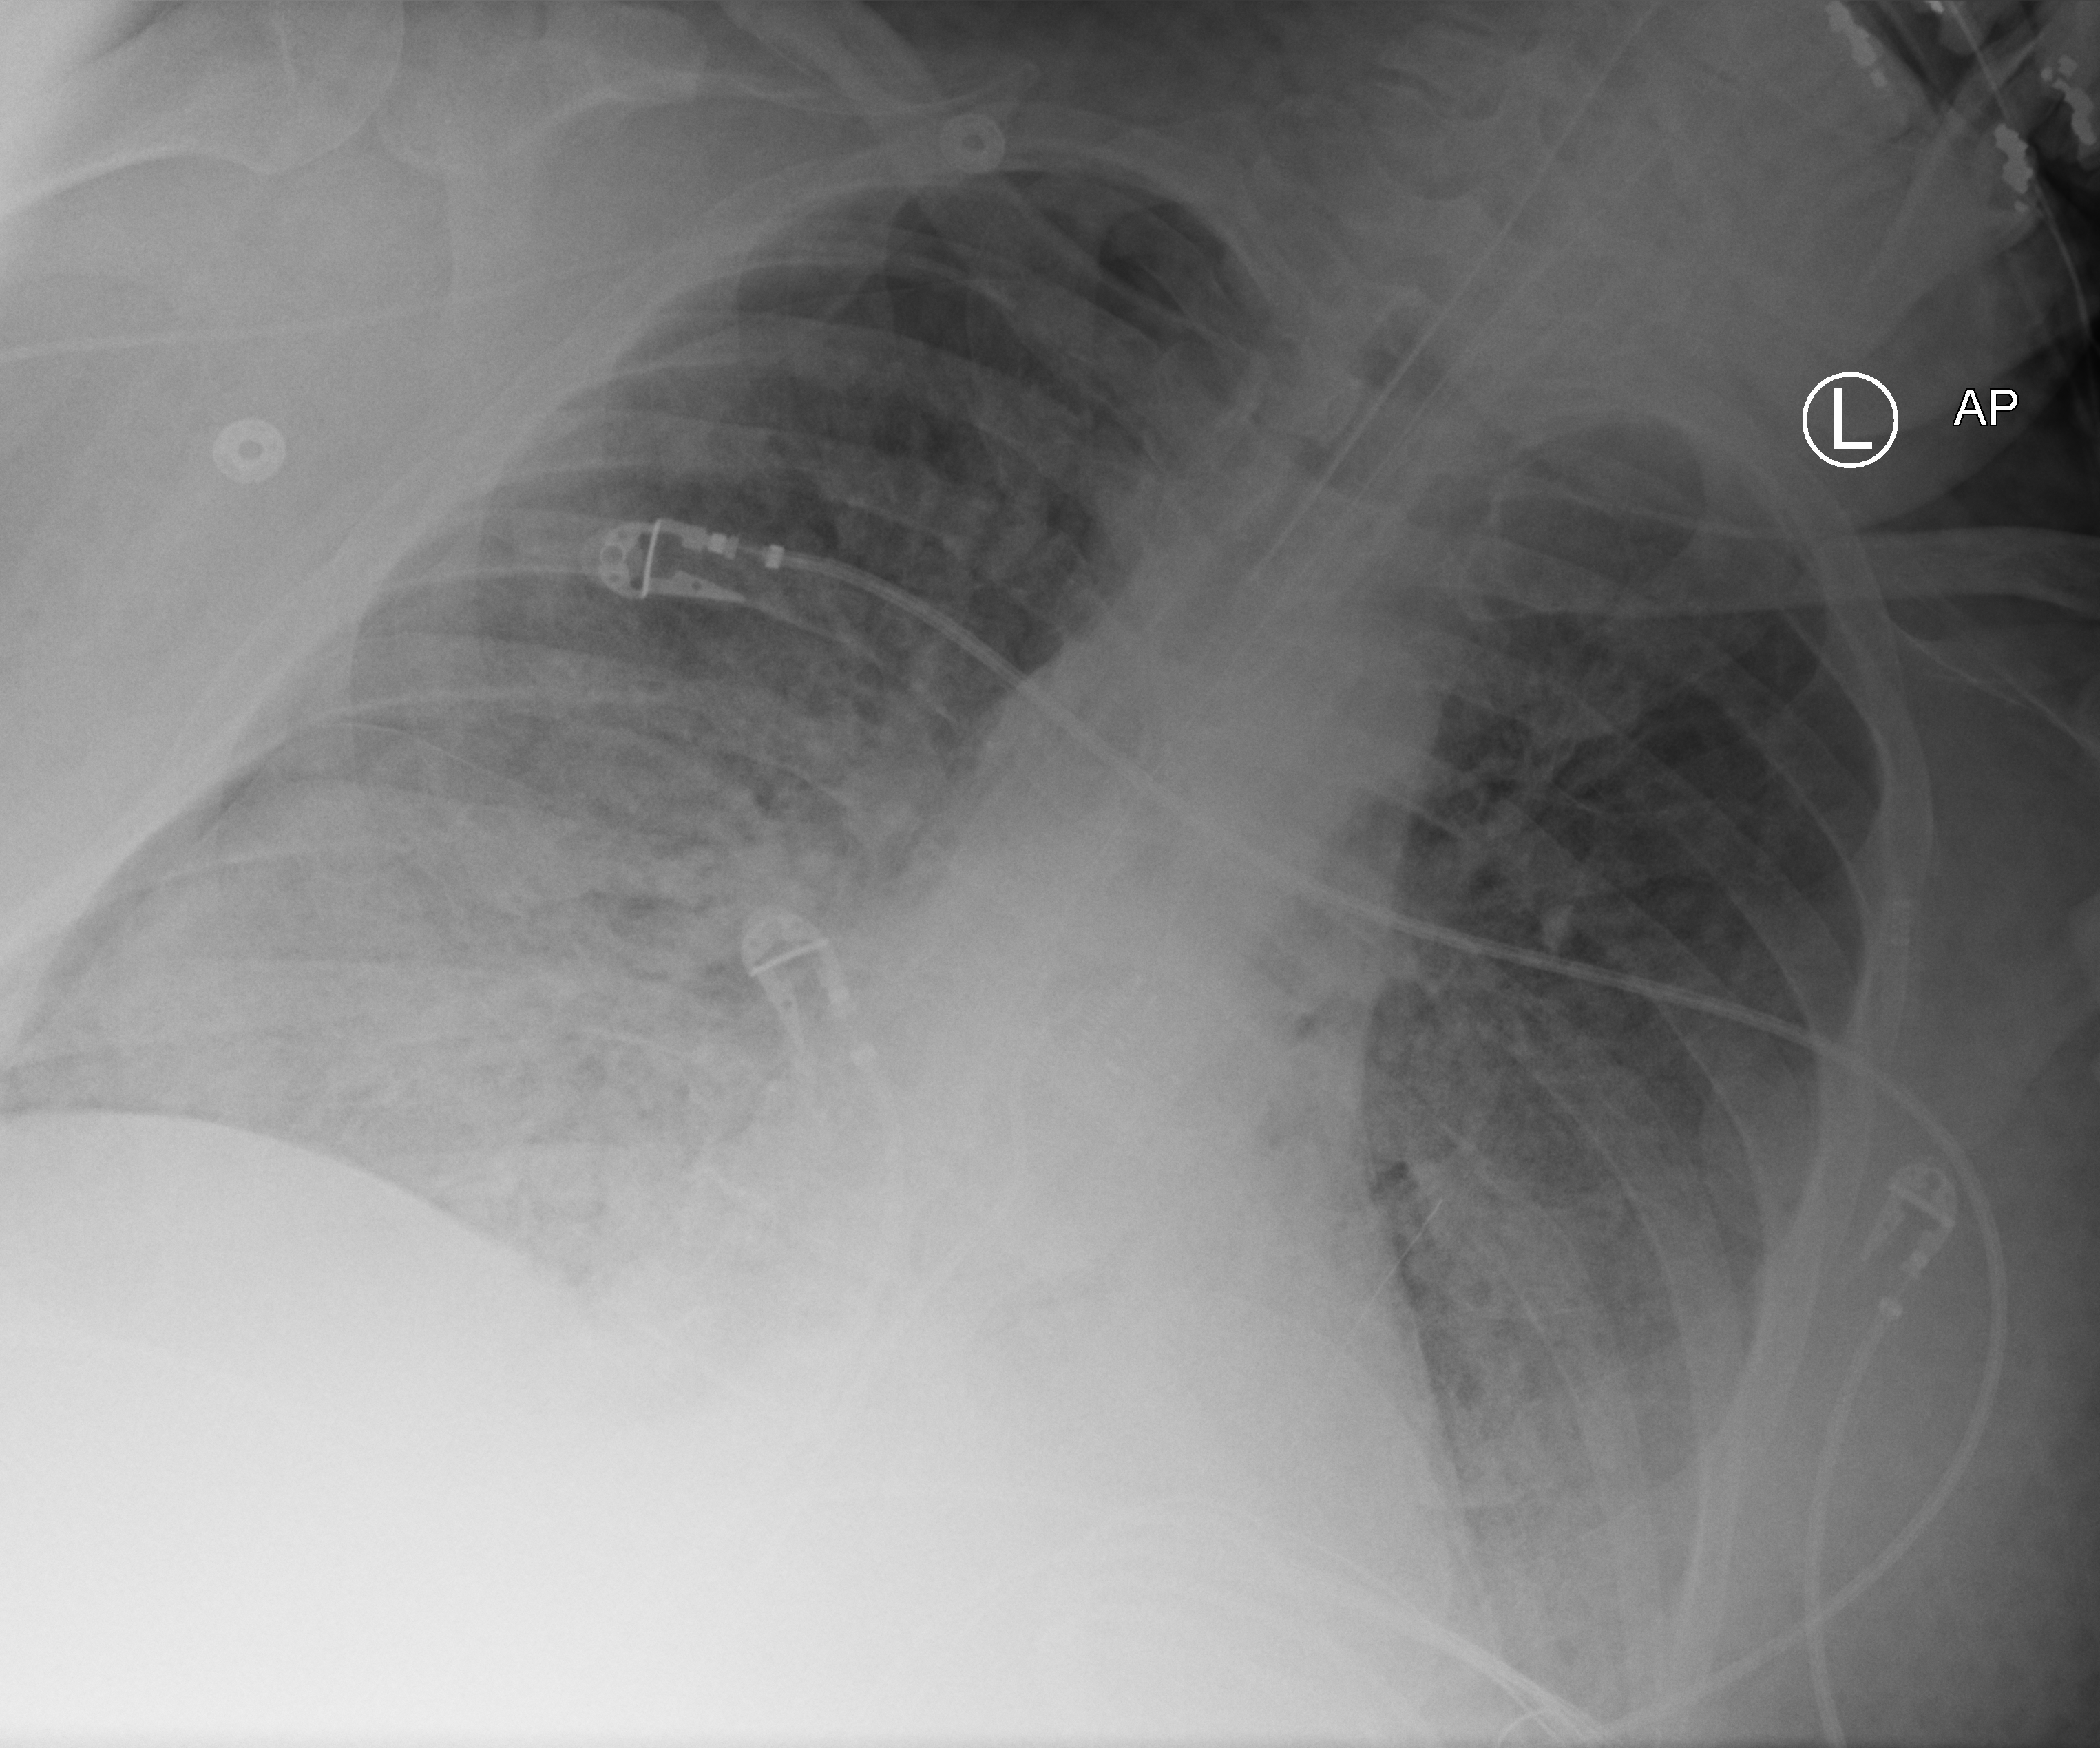
Portable chest radiograph; anteroposterior (AP) projection. Adult patient hospitalised with COVID-19, age 18–59 years.
Admission-level facts for this patient (not findings on this image; timing relative to this image not recorded): hypertension (admission record): yes.